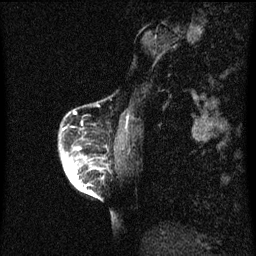
Breast MRI (dynamic contrast-enhanced), one sagittal slice; slice 14 of 60 in the series (ordered by position); dynamic contrast-enhanced series, image 2 of 3 at this slice position (ordered by acquisition); 1.5 T; TE 4.2 ms, TR 8 ms; 2 mm slice thickness; 256 × 256 image matrix. Female patient, age 56 years.
Structures marked on this image (semi-automatic segmentation, software-assisted and operator-edited):
- analysis volume of interest (the breast-tissue region the enhancement analysis was run in; not a lesion): bounding box (x1, y1, x2, y2) in pixels: (59, 122, 108, 199)
- tumour enhancement mask (voxels above the 70 % enhancement threshold inside the analysis volume of interest): (64, 148, 97, 197)